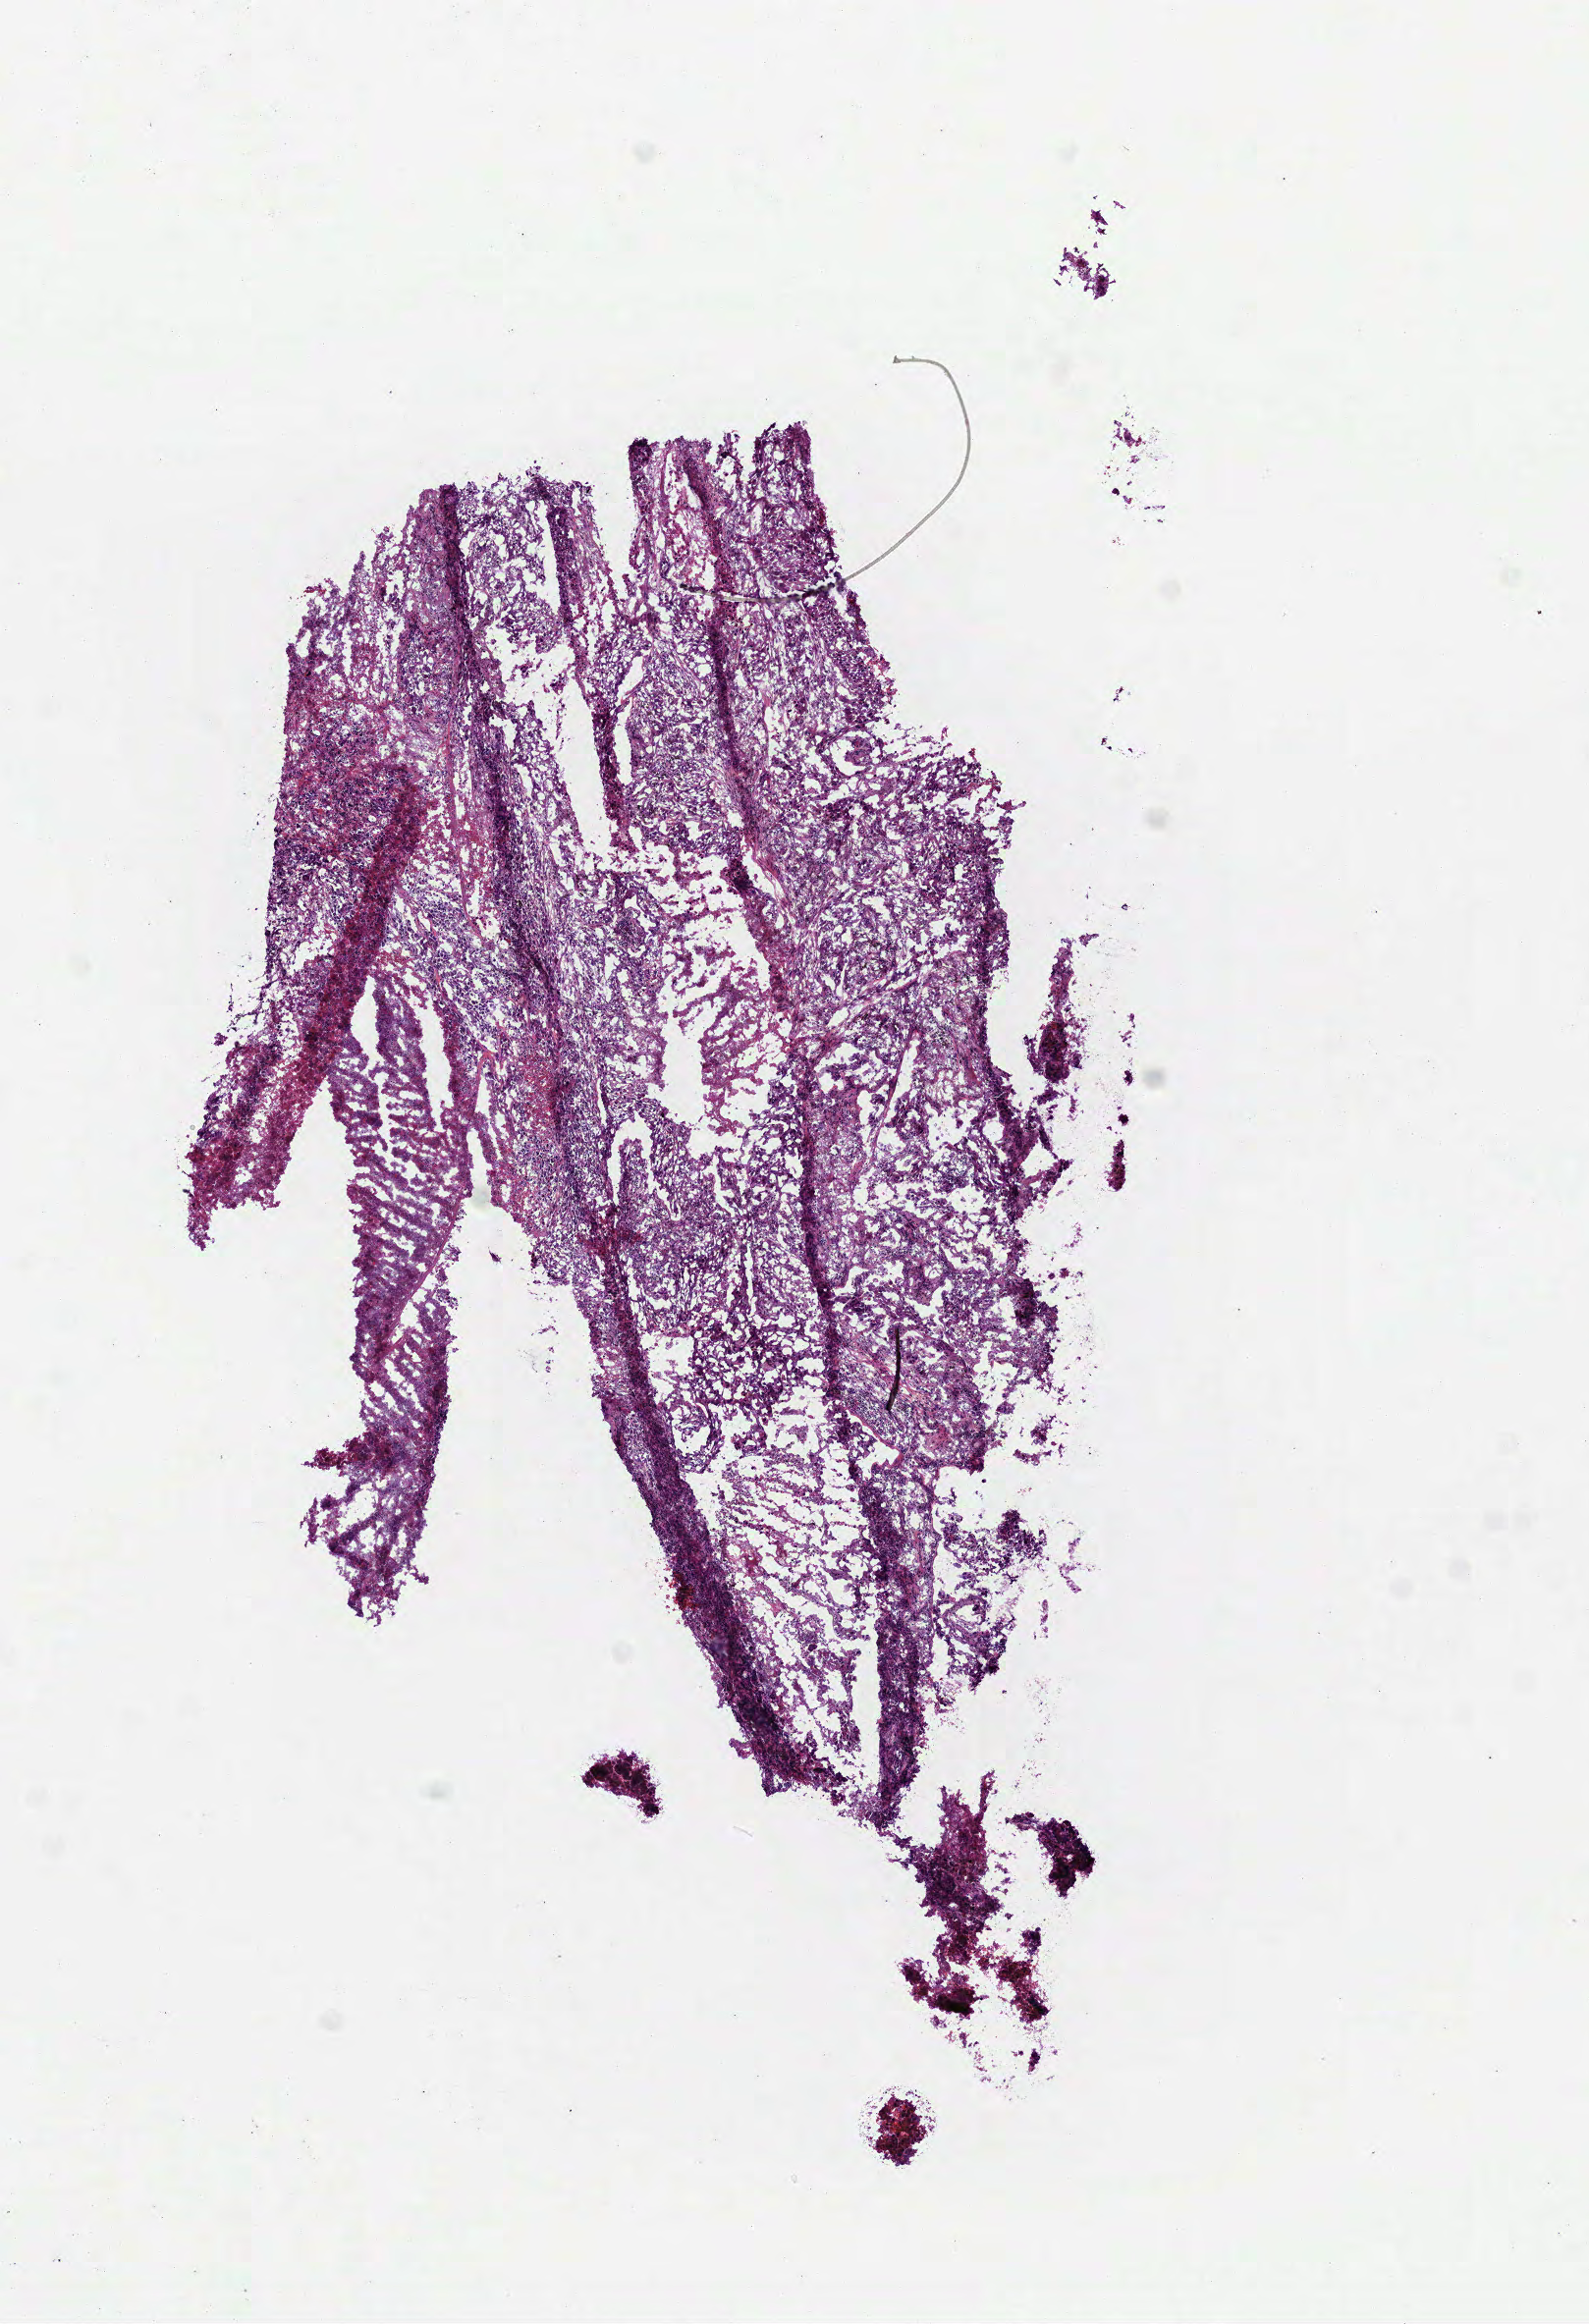
Whole-slide histology image, Hematoxylin and eosin (H&E) stained — shown as a low-resolution overview of the whole scanned area (about 6.5 x 9.5 mm), frozen section from the top of the tissue portion, primary tumour sample from the lung. Male patient; age at initial diagnosis 68 years. Slide review estimates, as recorded: tumour cells 85%, tumour nuclei 65%, normal cells 0%, stromal cells 5%, necrosis 10%.
Diagnosis: Squamous cell carcinoma, NOS (upper lobe, lung). AJCC pathologic stage: IIB (6th edition).